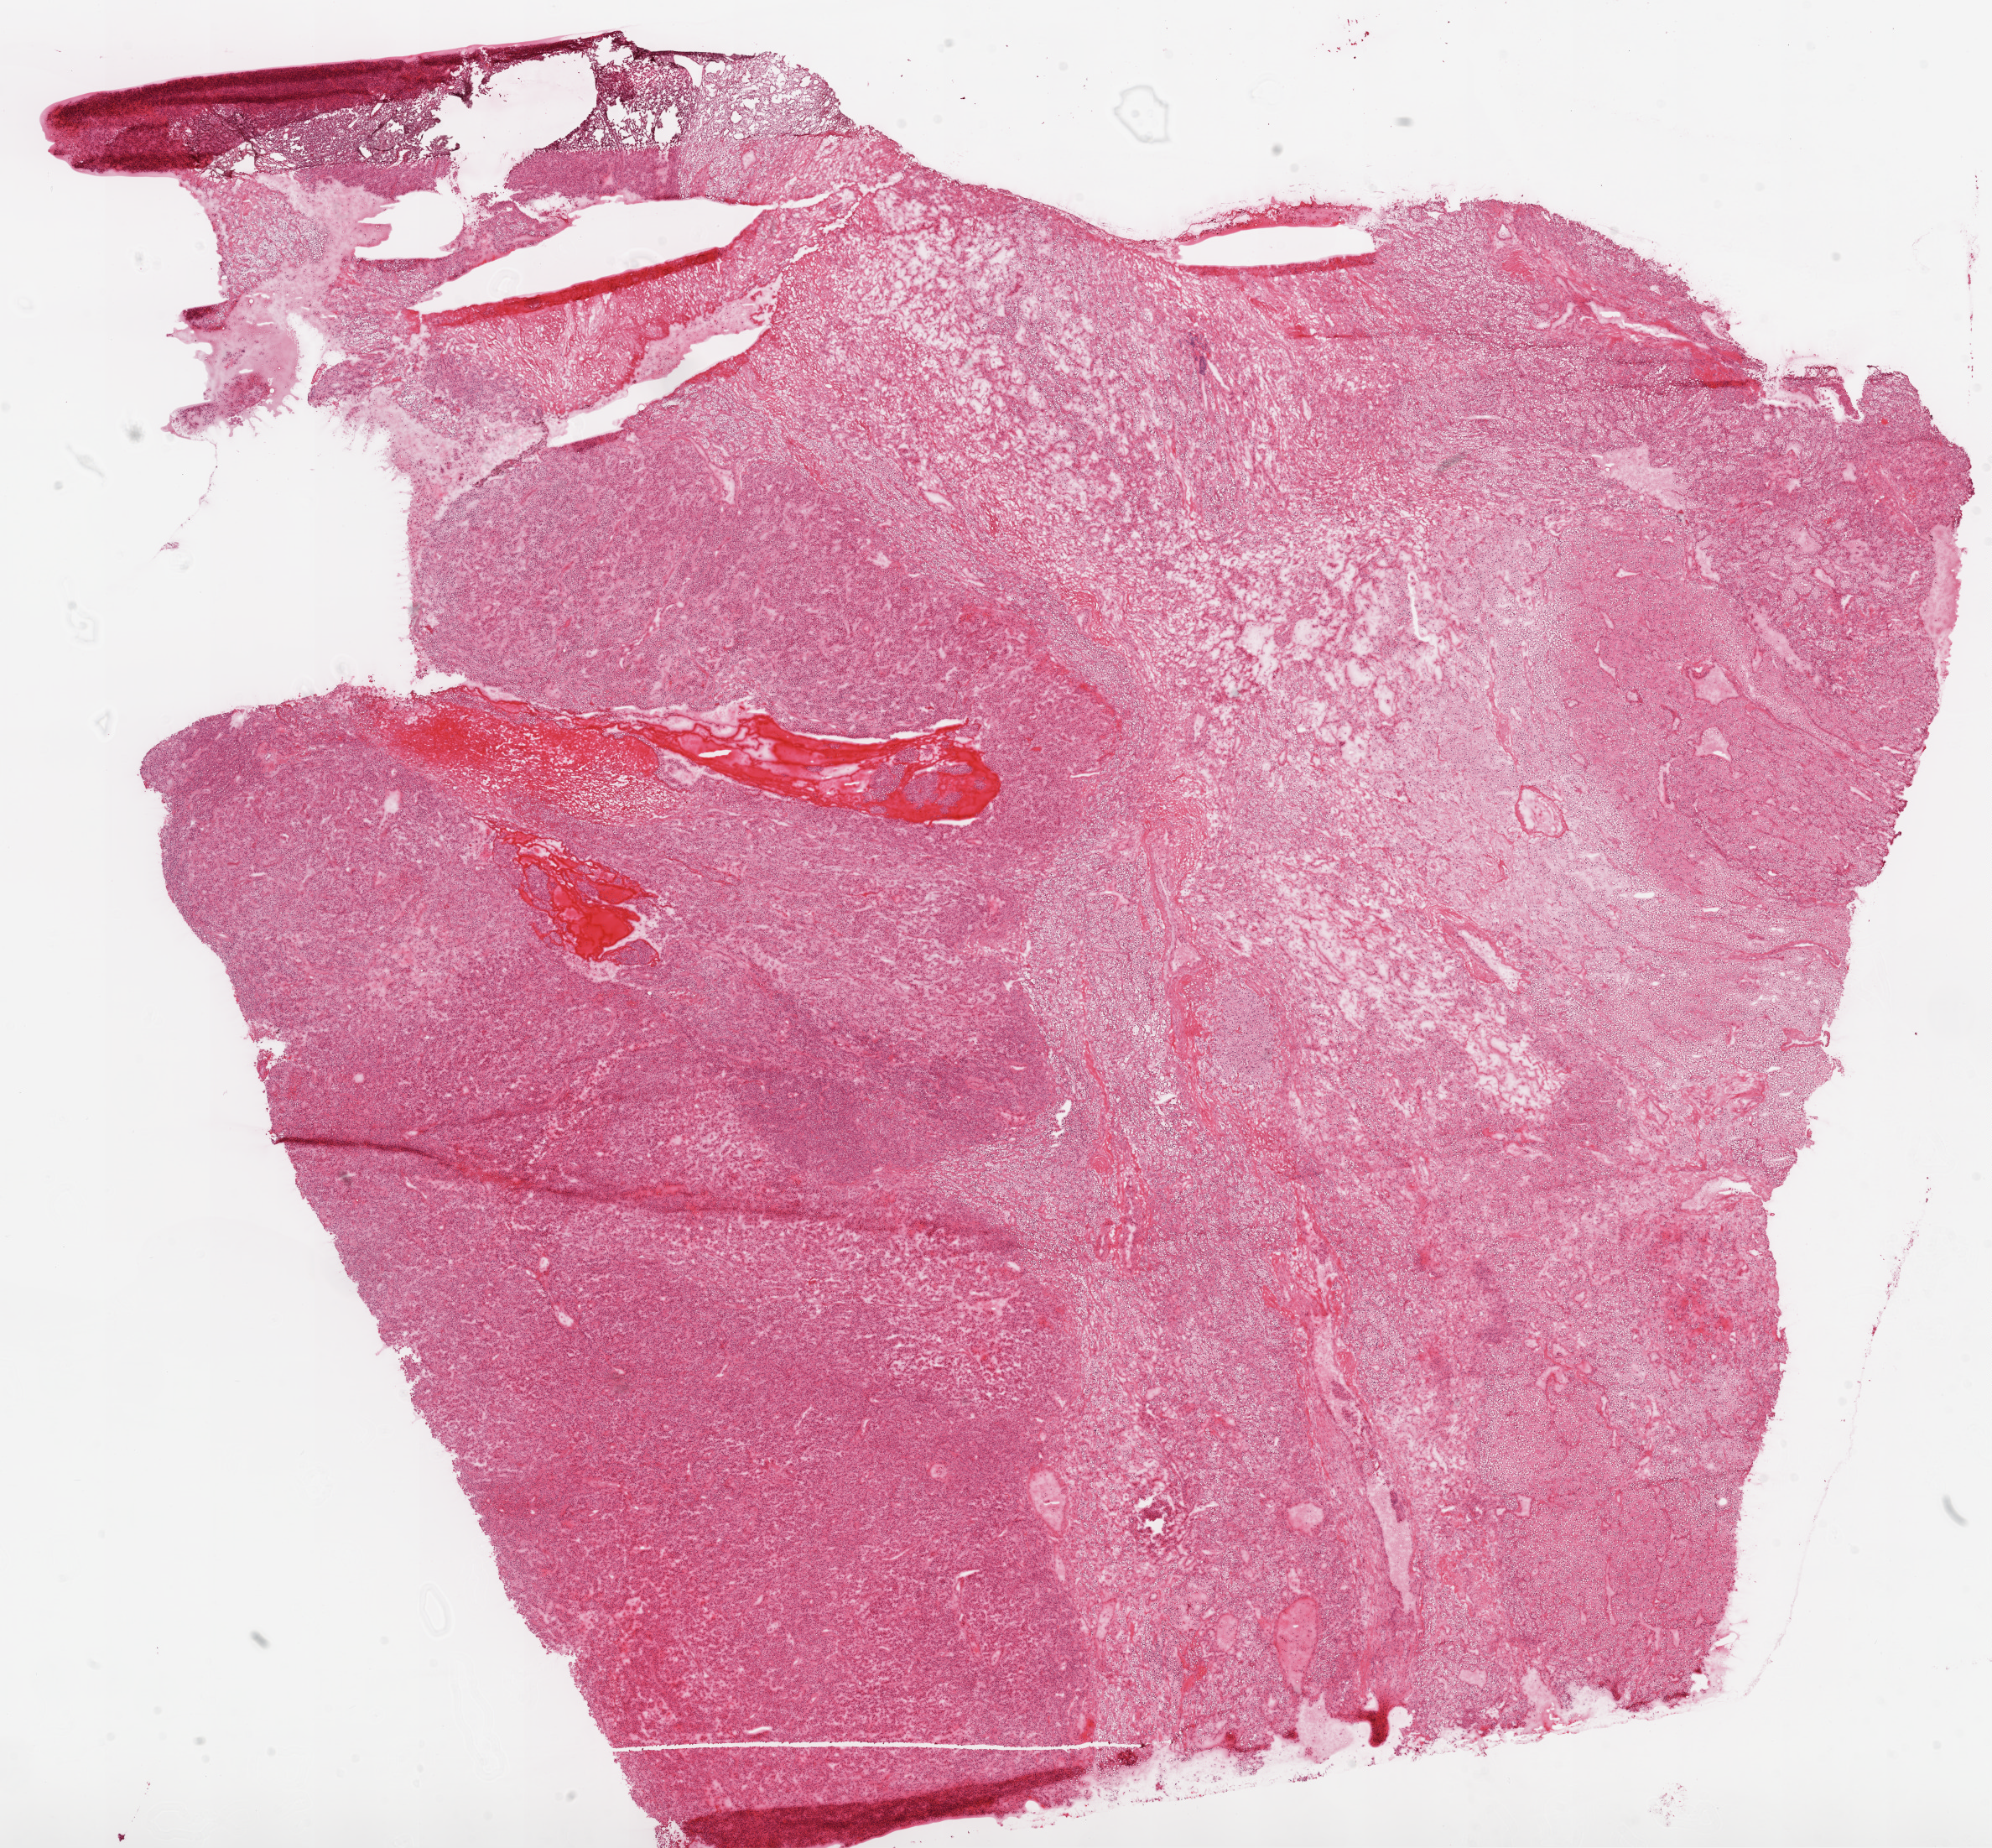
Whole-slide histology image, H&E, low-resolution overview of the scanned area, about 19.1 x 17.7 mm, frozen section from the top of the tissue portion, kidney, primary tumour sample. Female patient; age at initial diagnosis 53 years. Histologic grade: G2 (moderately differentiated). Pathologist review of this section (percent, as recorded): tumour cells 80%, tumour nuclei 90%, normal cells 0%, stromal cells 20%, necrosis 0%.
* AJCC pathologic stage: I
* pathologic diagnosis: Clear cell adenocarcinoma, NOS
* lymph nodes positive (case pathology): 0 of 3 examined